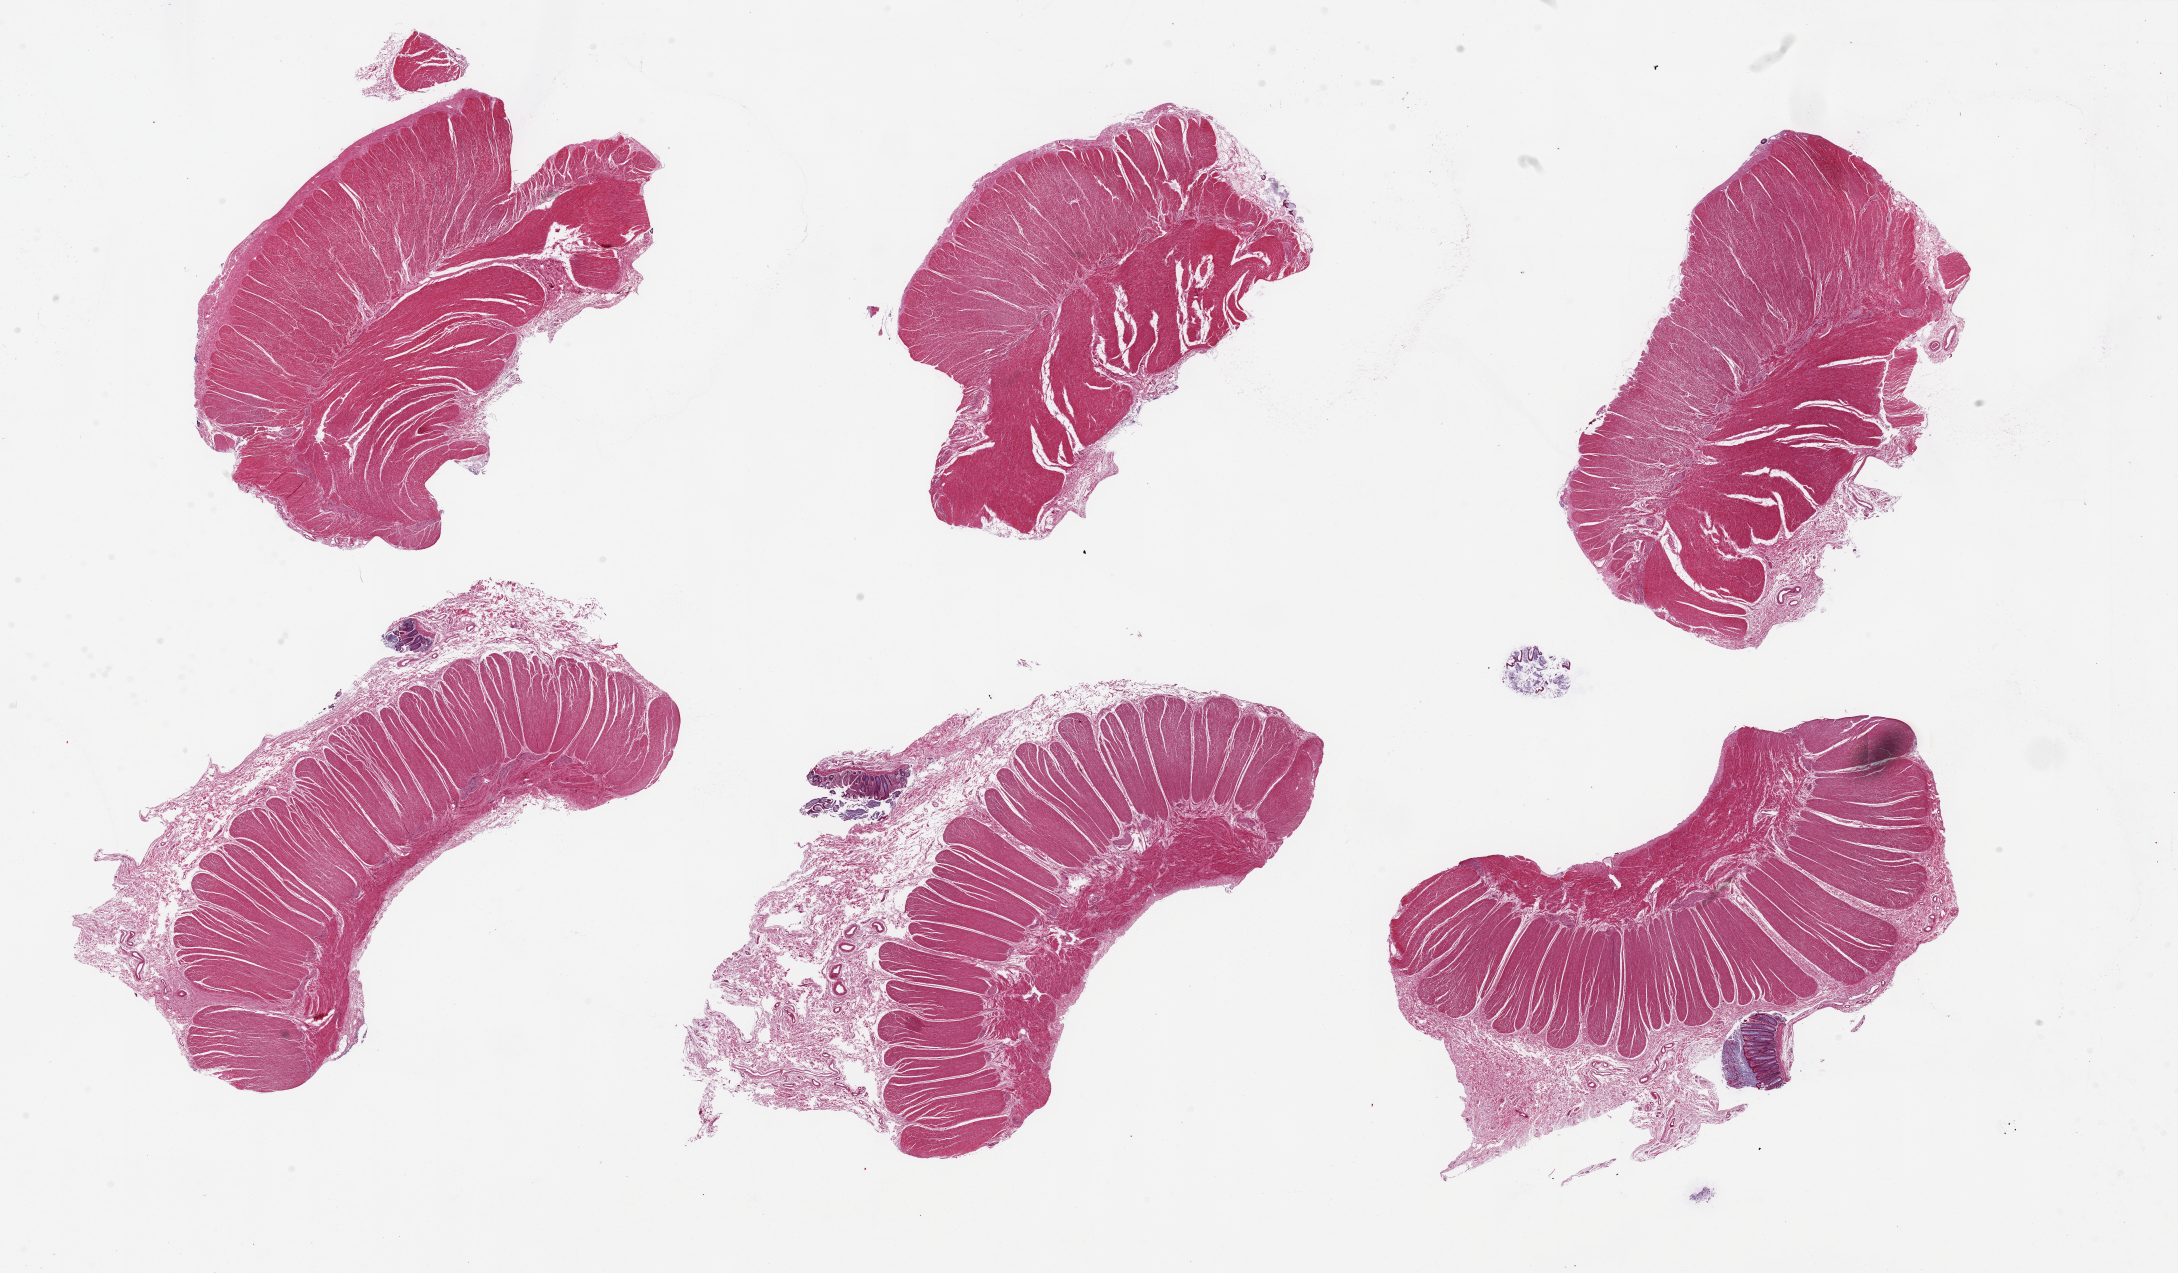
Hematoxylin and eosin (H&E) whole-slide image, whole scanned area (about 34.5 x 20.1 mm) shown as a low-resolution overview; PAXgene-fixed paraffin-embedded (PFPE) section; section of sigmoid colon (target tissue); tissue donor sample.
Pathologist's review note for this sample: 6 pieces, up to 11.5x6mm; ~90% target muscularis, good specimens.